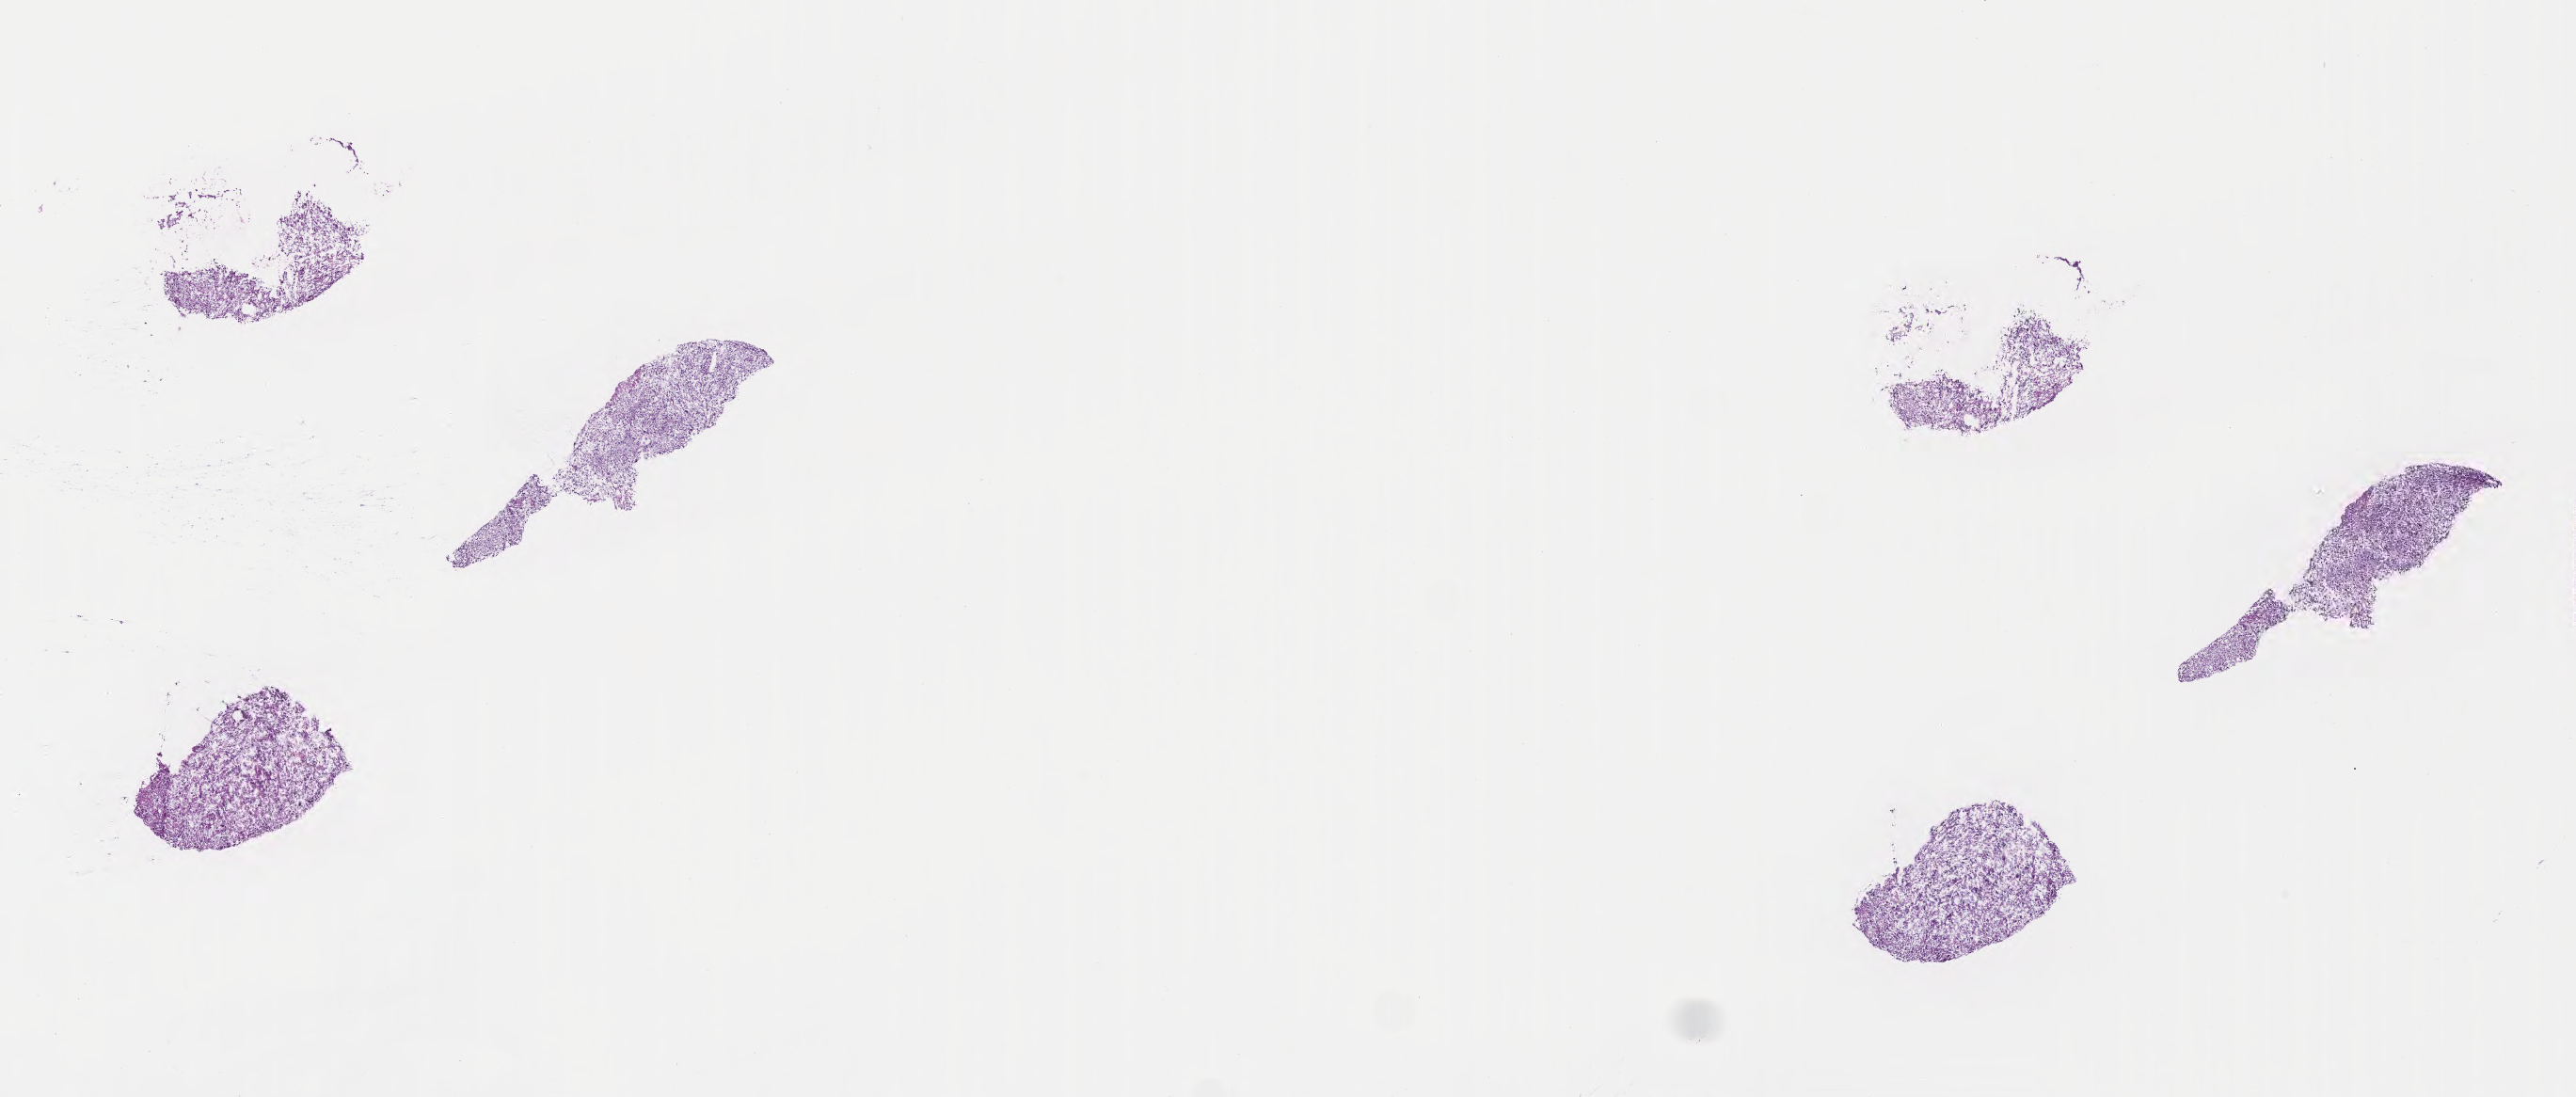
H&E whole-slide image, a low-resolution overview of the entire scanned area, about 22.1 x 9.4 mm. Frozen section. Specimen: primary tumor. Site: brain. Female, age 49 years at initial diagnosis. Composition of this section per pathologist review: tumor cells 86%, tumor nuclei 93%, stromal cells 4%, necrosis 4%, normal cells 6%. Infiltration values recorded for this section: lymphocyte infiltration 0%, monocyte infiltration 0%, neutrophil infiltration 0%.
Diagnosis: Glioblastoma, NOS. Section: top of the tissue portion.